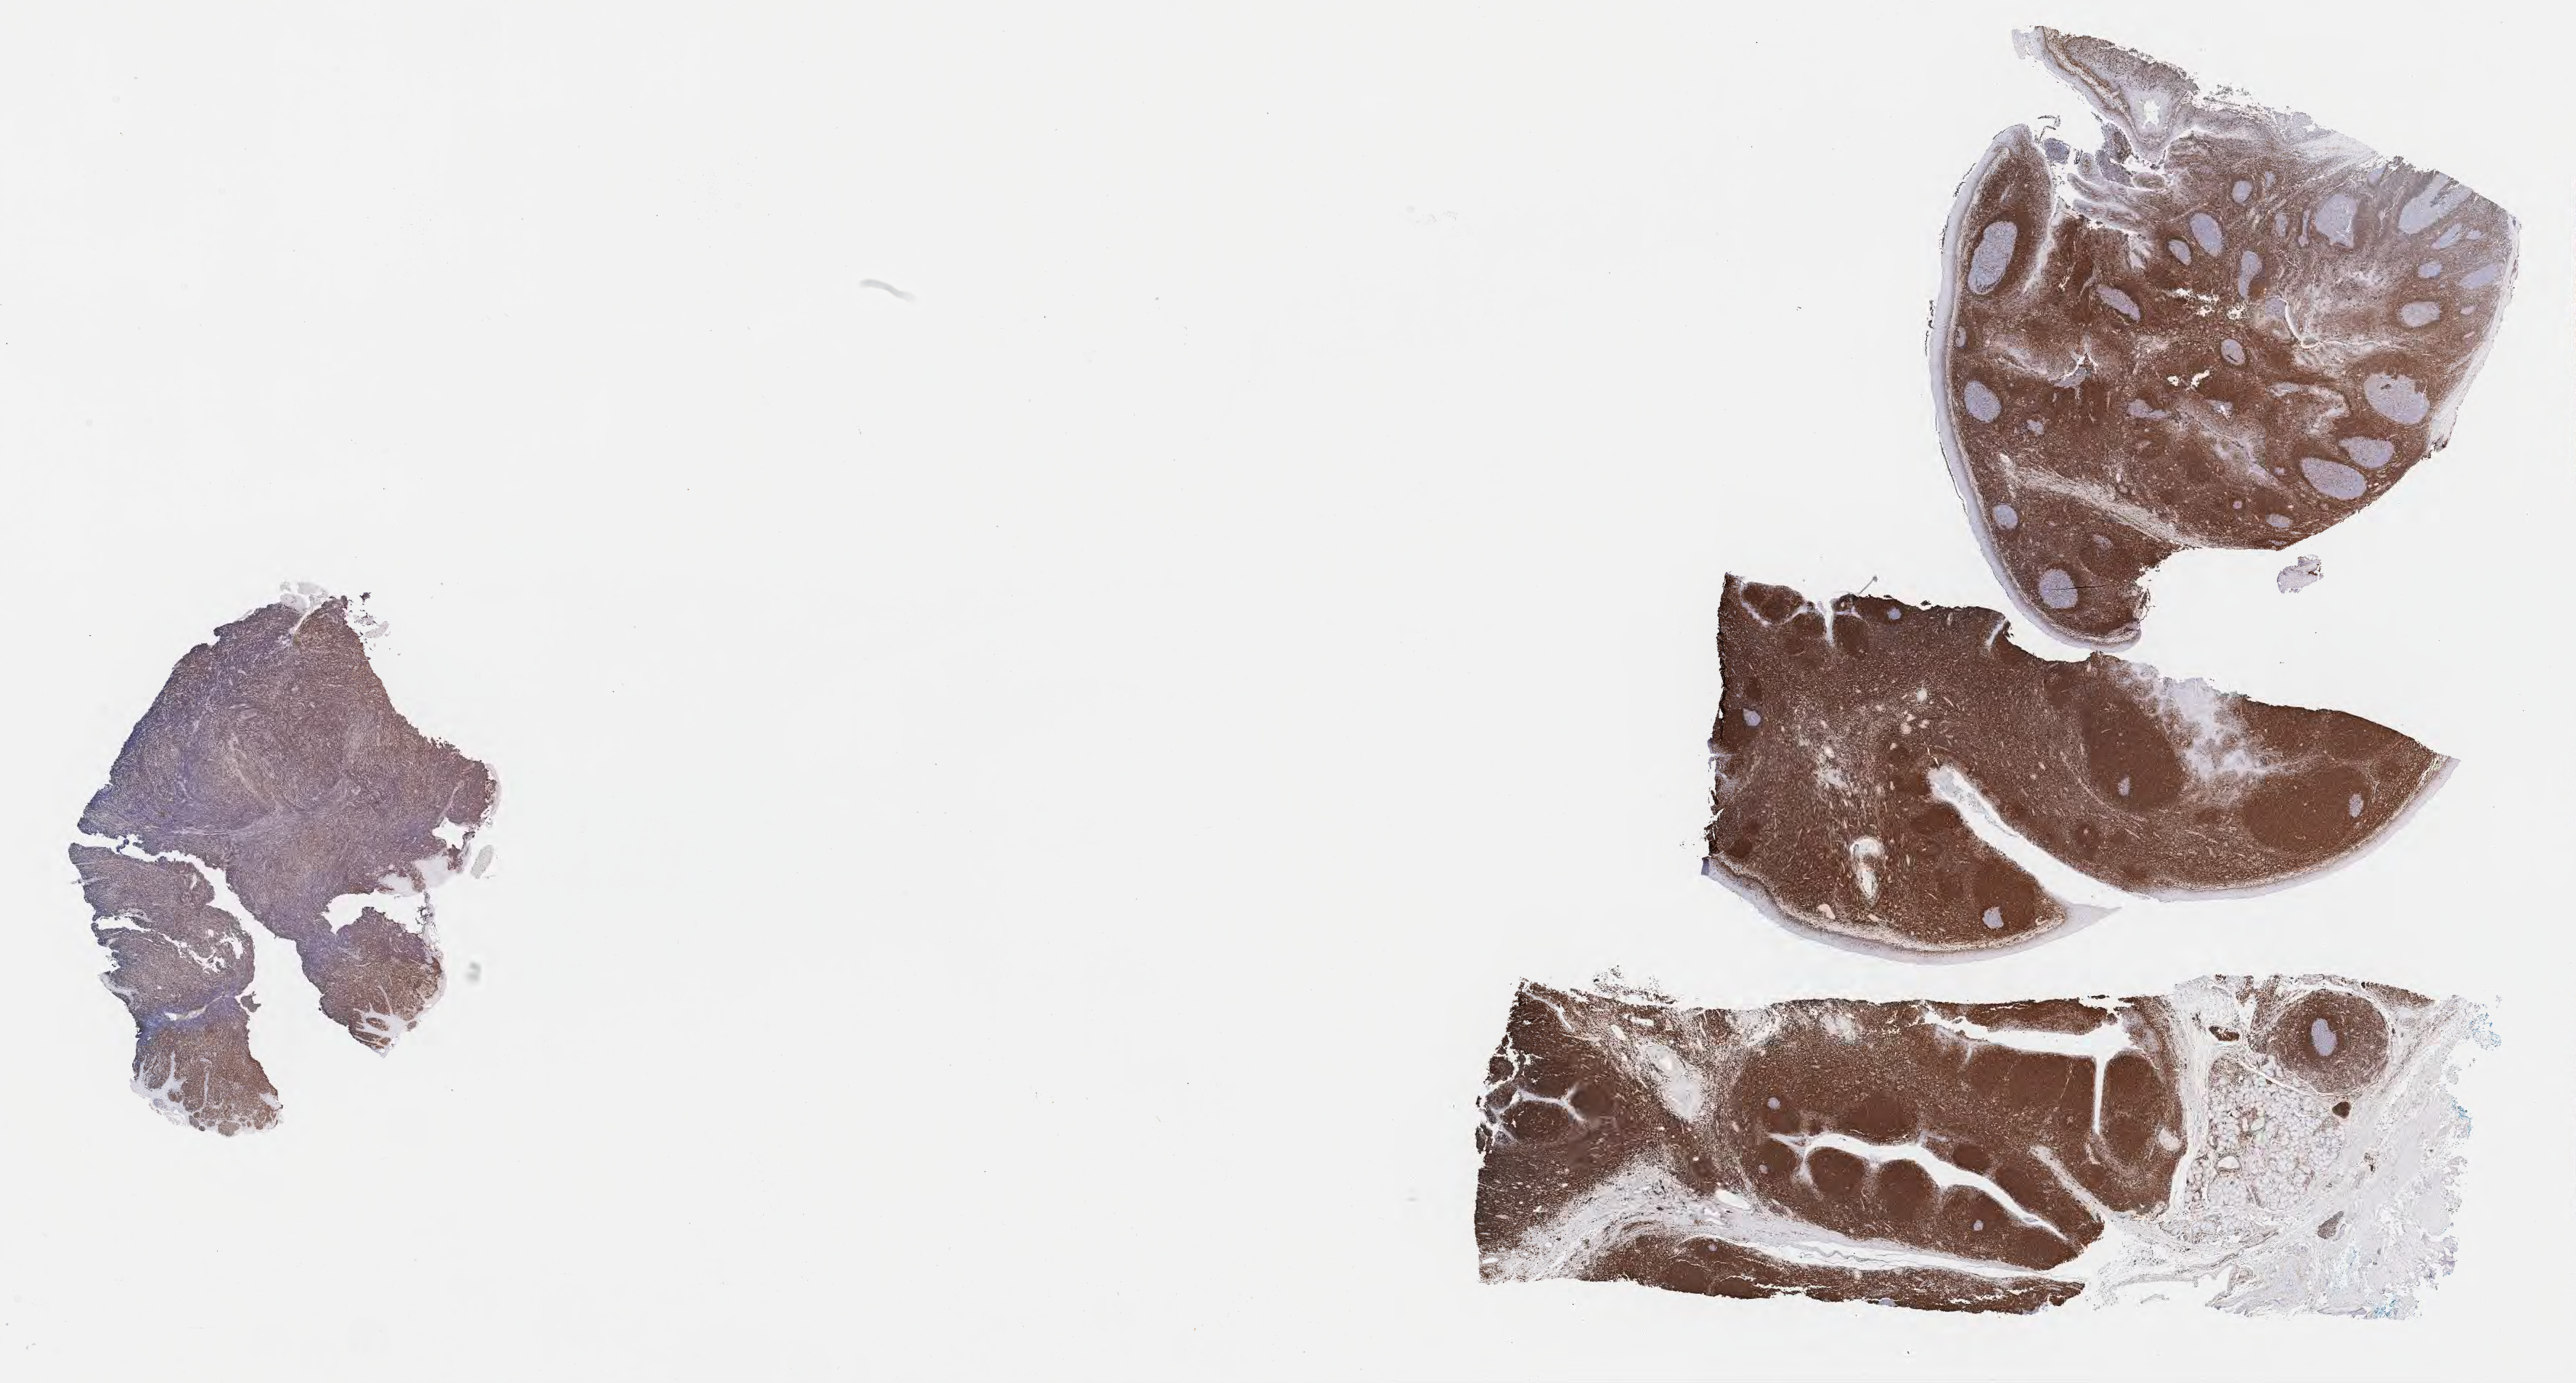
Immunohistochemistry (IHC) whole-slide image stained for BCL2 — shown as a low-resolution overview of the whole scanned area (about 28.7 x 15.4 mm). Tumor tissue. Anatomic site: cranium. Patient: male, age 11 years.
- histologic diagnosis: Diffuse large B-cell lymphoma, NOS